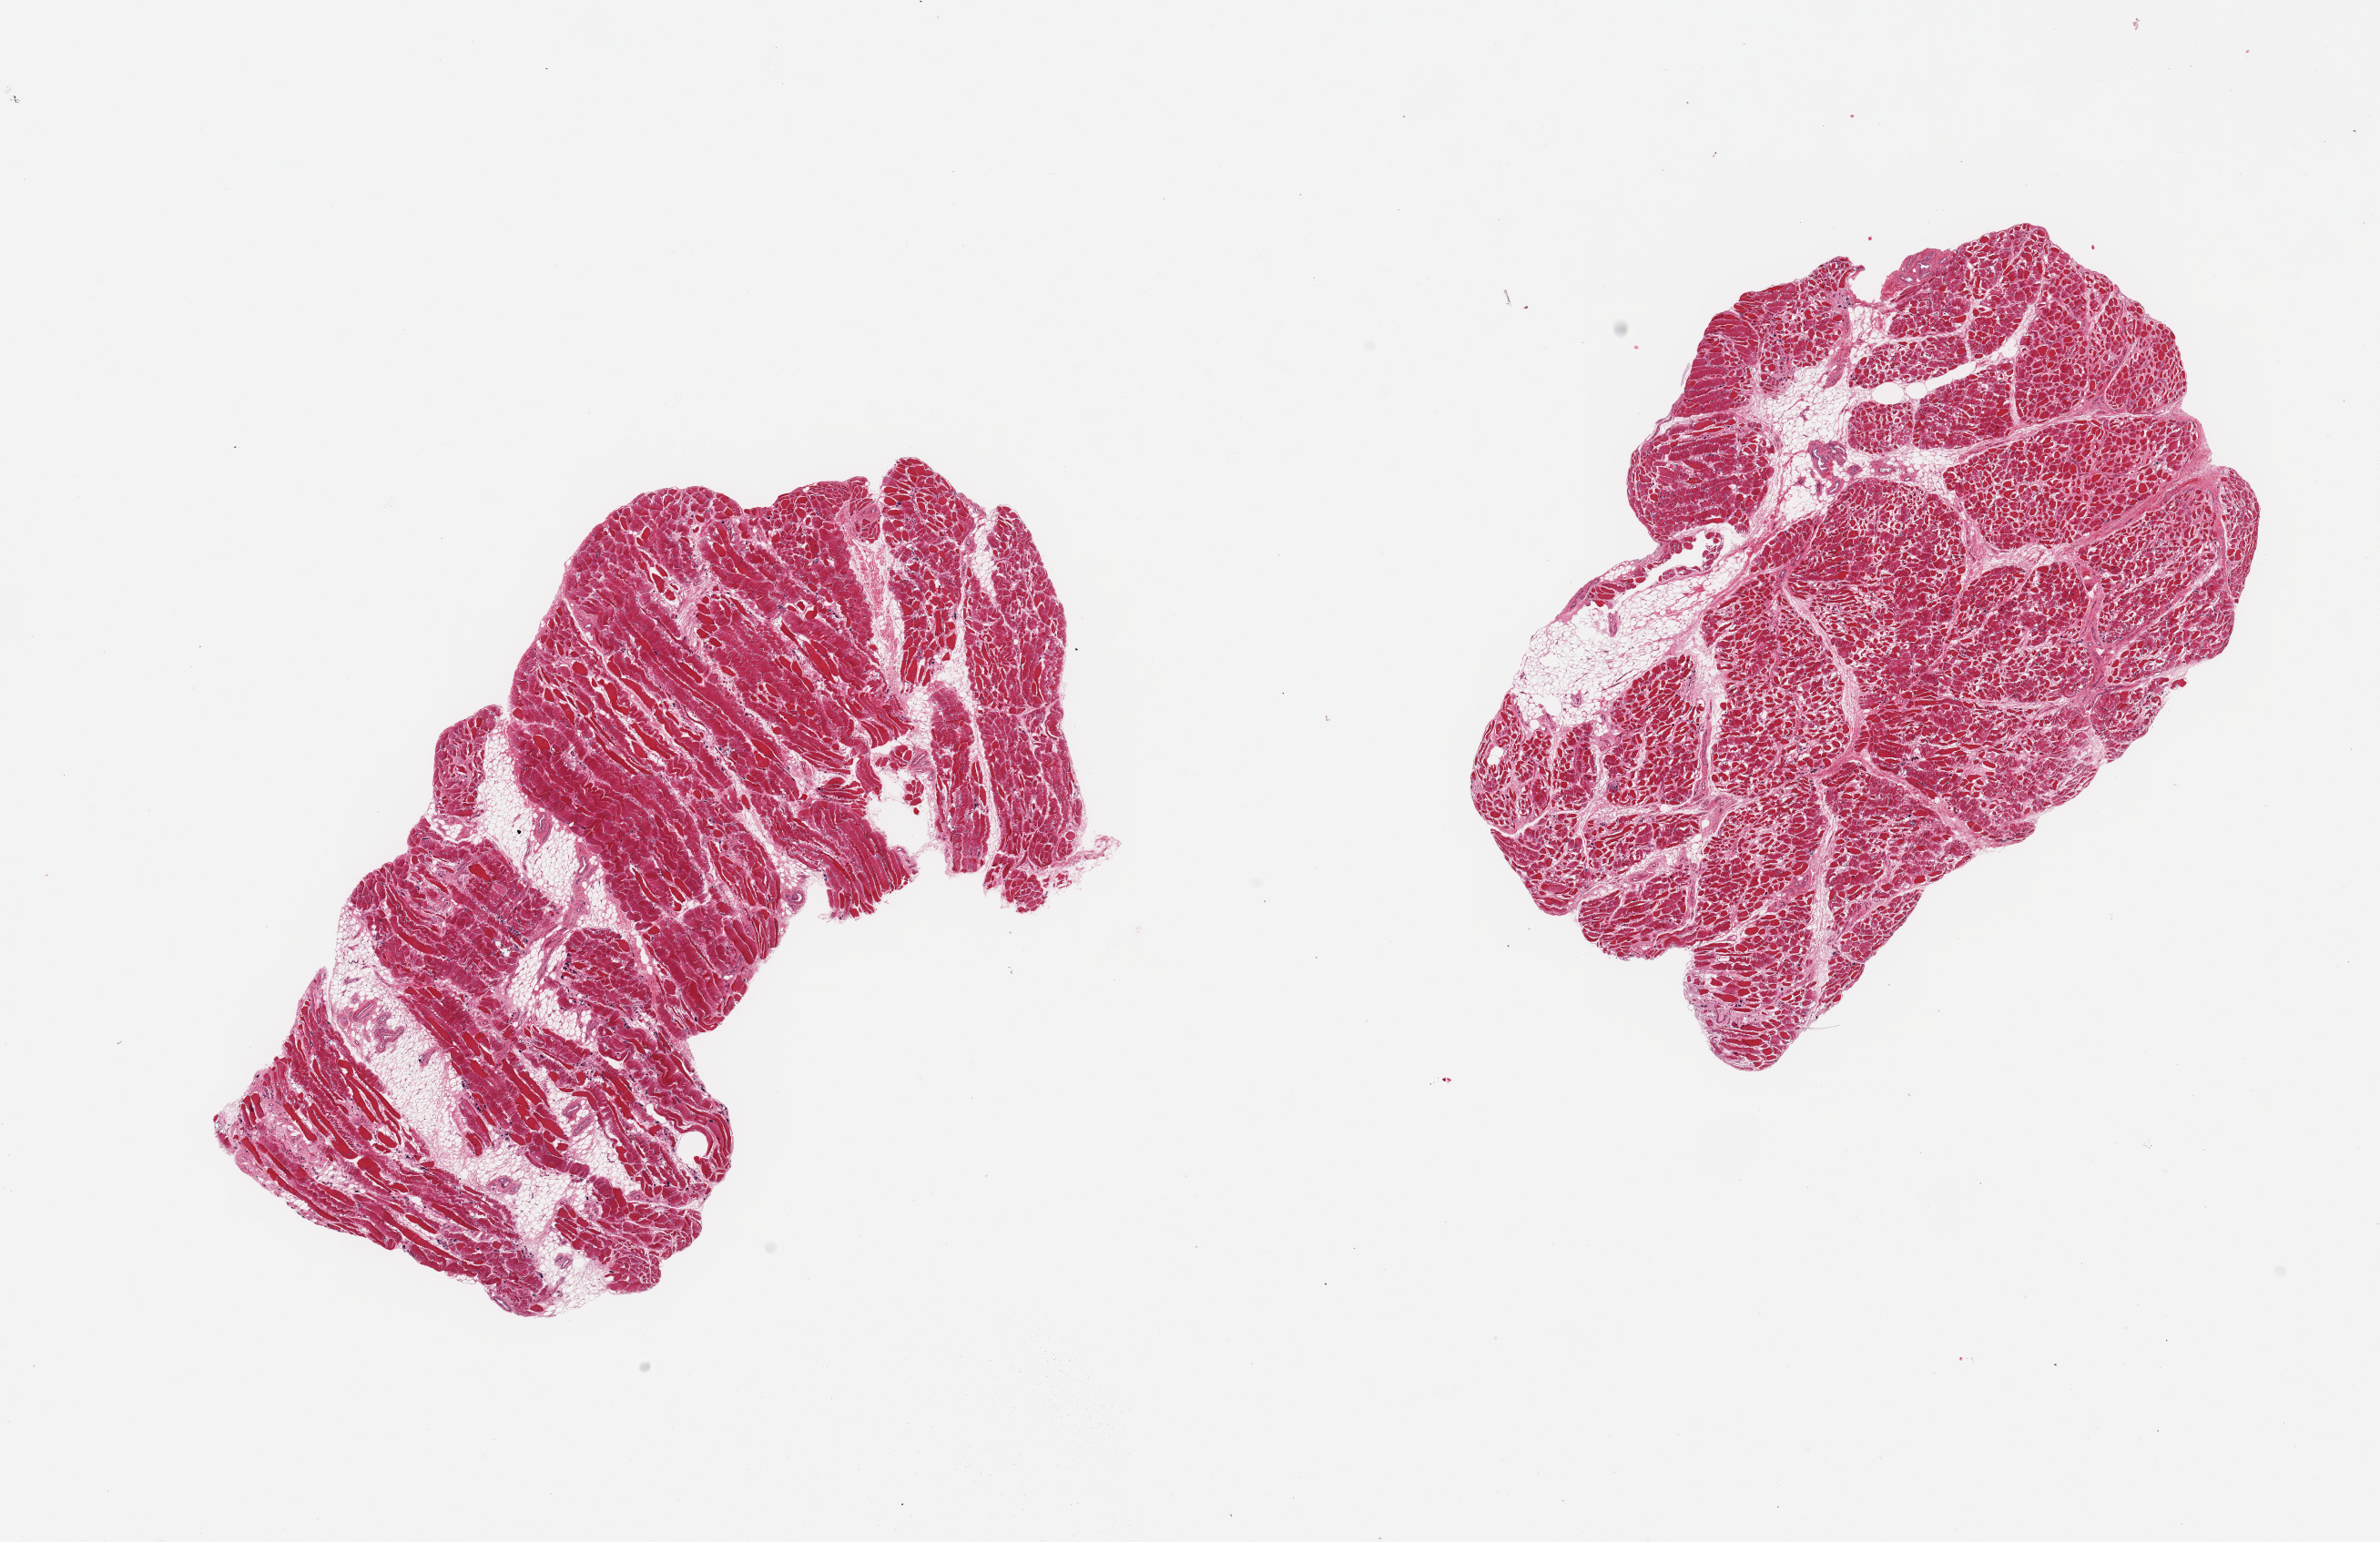
H&E whole-slide image, shown as a low-resolution overview of the whole scanned area (about 20.7 x 13.4 mm, slide scanned at 20x), PAXgene-fixed paraffin-embedded (PFPE) section, section of skeletal muscle (target tissue), tissue donor sample. Male donor.
Review note (as recorded): 2 pieces; ~10-15% internal fat, some atrophy.